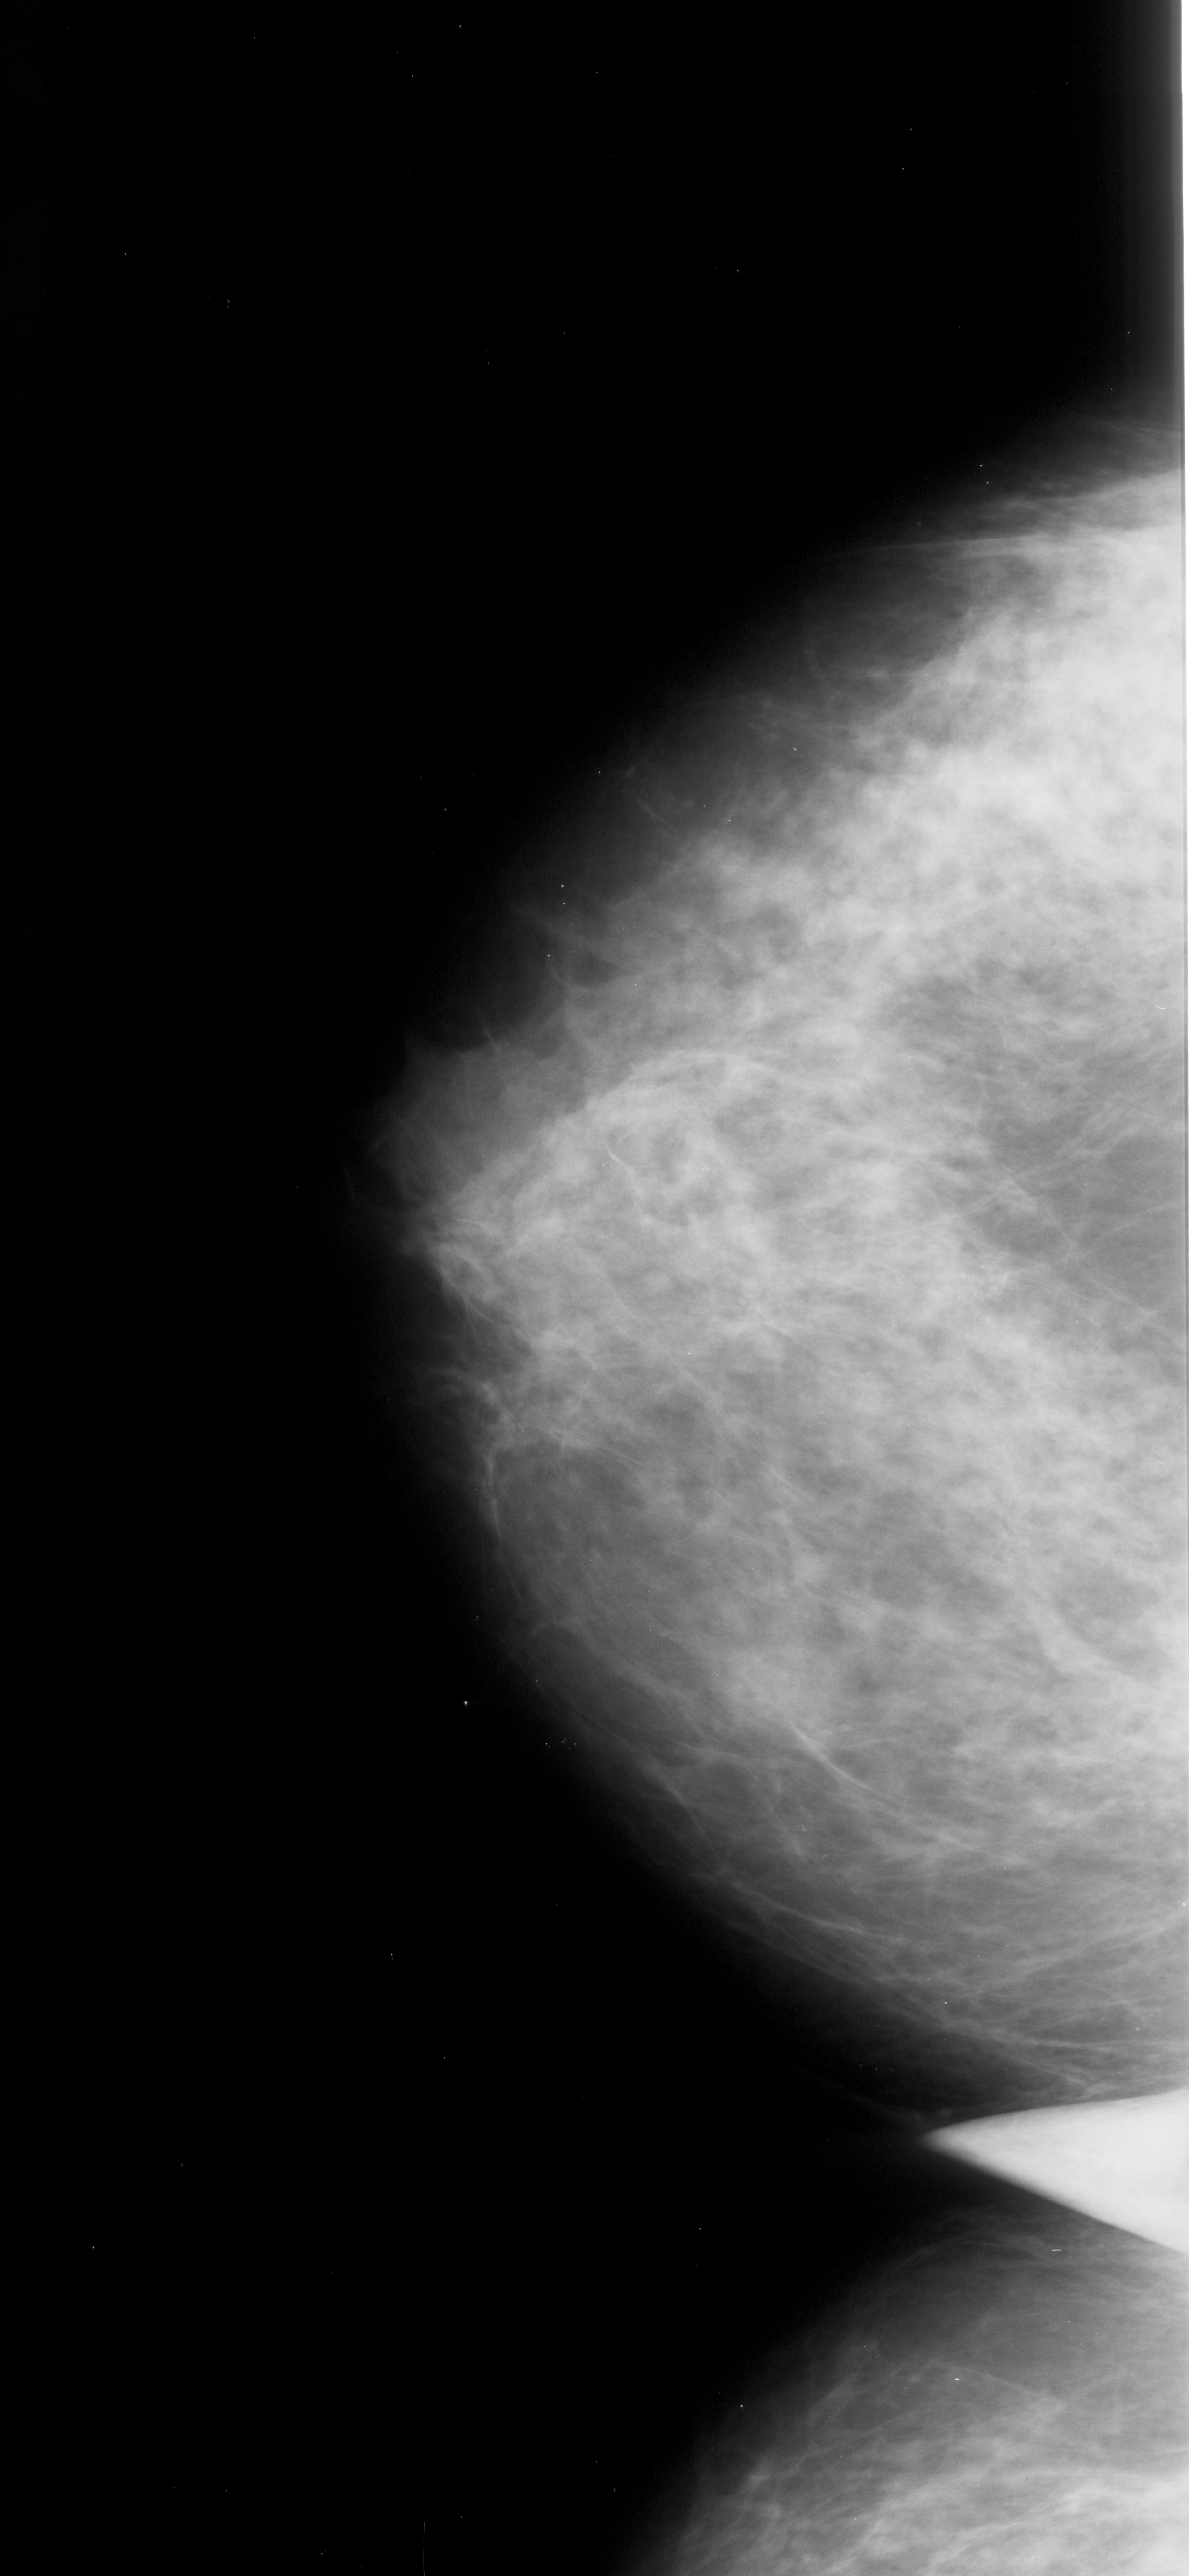
Scanned film-screen mammogram; left breast; craniocaudal (CC) view; BI-RADS breast density category 3 (scale 1–4).
- Calcifications, morphology pleomorphic, distribution clustered; BI-RADS assessment category 4; subtlety rating 1 on a 1 (subtle) to 5 (obvious) scale; pathology result (as recorded, not read from the image): malignant.